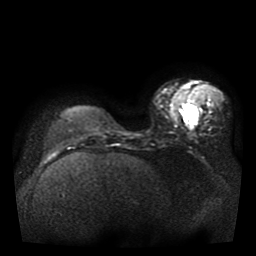
Breast MRI, one axial slice; slice 13 of 41 in the series (ordered by position); diffusion-weighted series; image 2 of 4 stored at this slice position (different b-values; order by instance number); 1.5 T; 5 mm slice thickness; 256 × 256 image matrix, field of view 330 × 330 mm. Female patient.
Annotated regions visible in this slice (expert manual segmentation):
- tumour on diffusion-weighted imaging: bounding box [x1, y1, x2, y2] px = [186, 107, 198, 122]